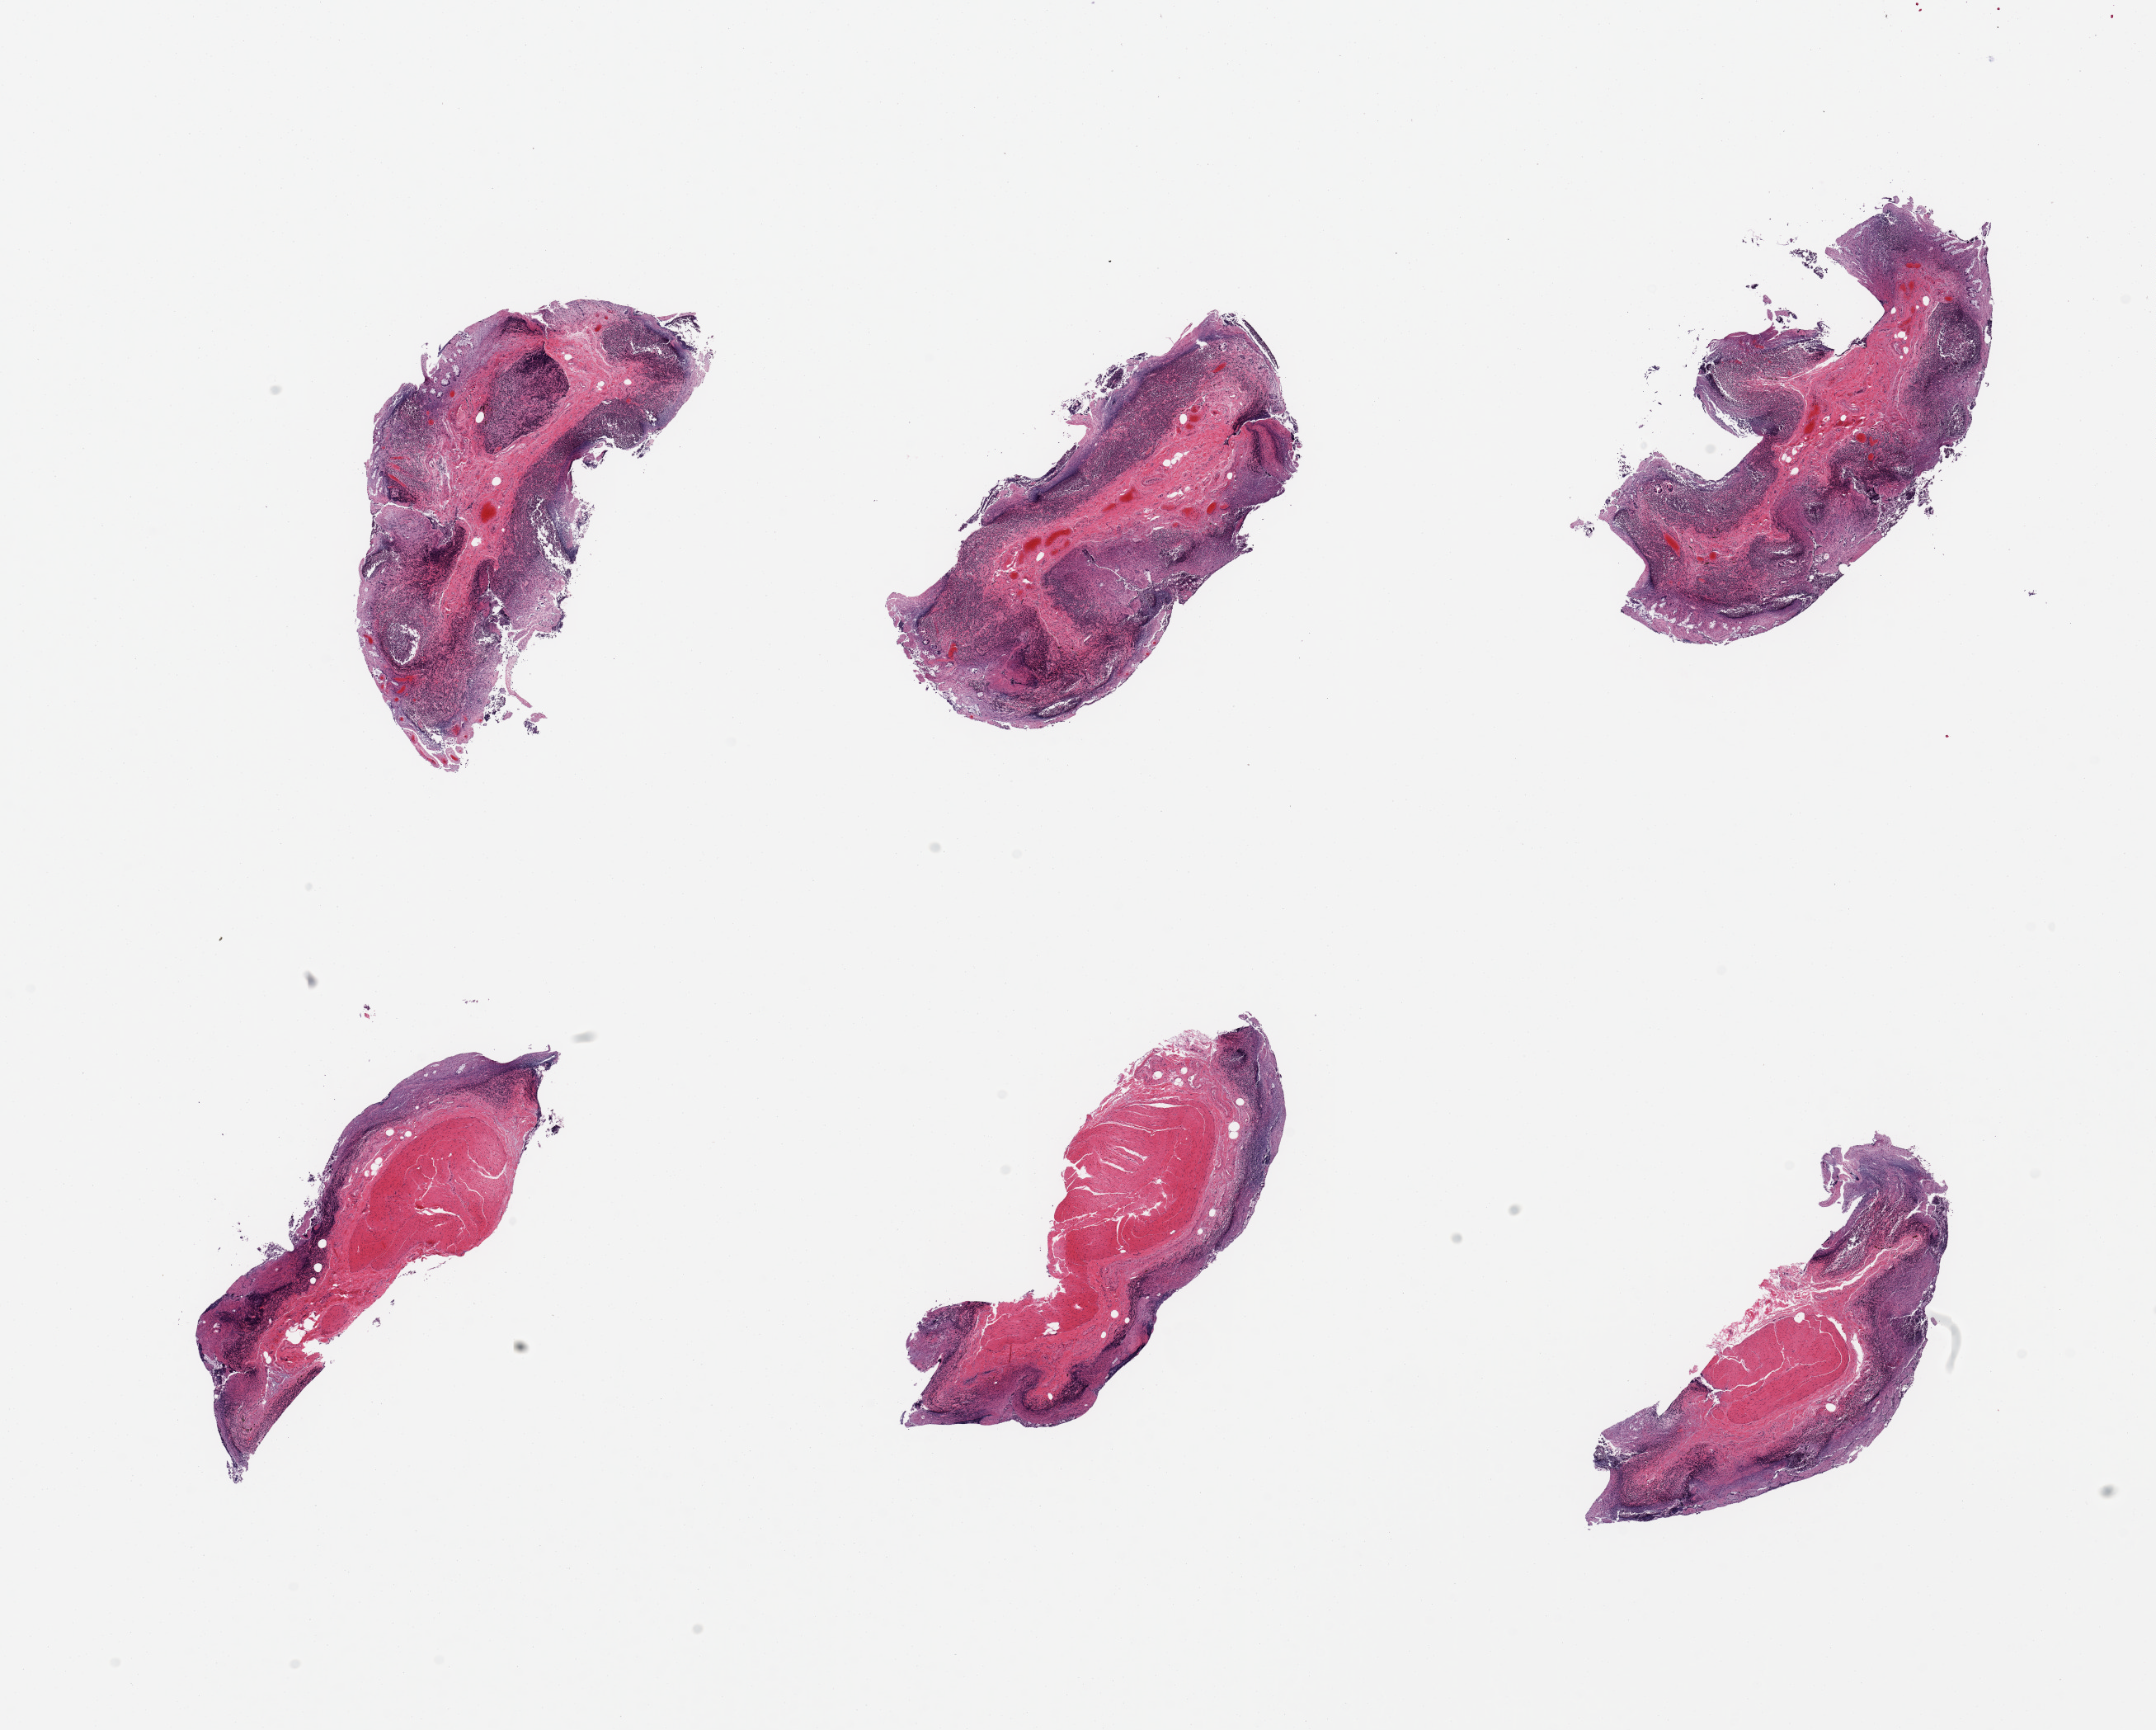
Whole-slide image, H&E stain — whole scanned area (about 20.7 x 16.6 mm) shown as a low-resolution overview; PAXgene-fixed paraffin-embedded (PFPE) section; section of ileum (target tissue); tissue donor sample. Donor: male.
* pathologist's review note for this sample: 6 pieces: abundant but autolyzed lymphoid tissue; muscularis present on 3 pieces